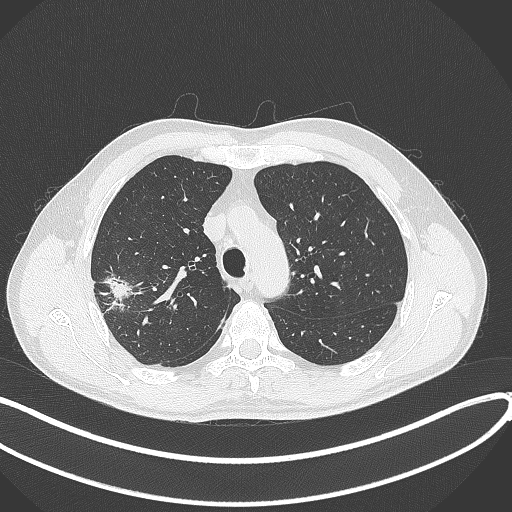
Chest CT, one axial slice. Position 311 of 381 along the scan axis. Reconstruction kernel B70f. Lung window (W 1500 / L -600 HU). 1 mm slice thickness. 512 × 512 image matrix. Male patient, age 62 years. Case-level facts recorded for this patient, not image findings: clinical TNM (as recorded): T1c N0 M0; histopathological grade: G2-3.
Outlined on this slice (rectangle marked by the reading radiologist):
- lung tumour (recorded histology: adenocarcinoma): bounding box [x1, y1, x2, y2] px = [101, 269, 136, 303]